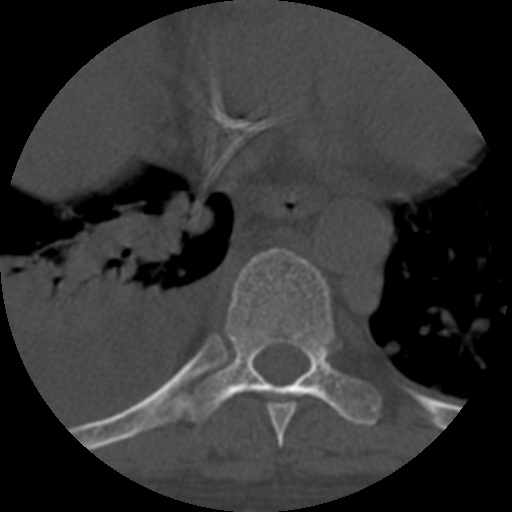
CT including the spine, one axial slice. Slice 382 of 708 in the series (ordered by position). Reconstruction kernel STANDARD. One of 3 acquisitions stored at this slice position. Bone window (W 1800 / L 400 HU). 512 × 512 image matrix, field of view 160 × 160 mm. Patient age 55 years. From the clinical record (not read from this slice): primary cancer: colon.
Annotated regions visible in this slice (semi-automatically segmented with operator editing):
- T8 vertebra: bounding box [x1, y1, x2, y2] px = [267, 403, 296, 447]
- T9 vertebra: [182, 248, 381, 426]